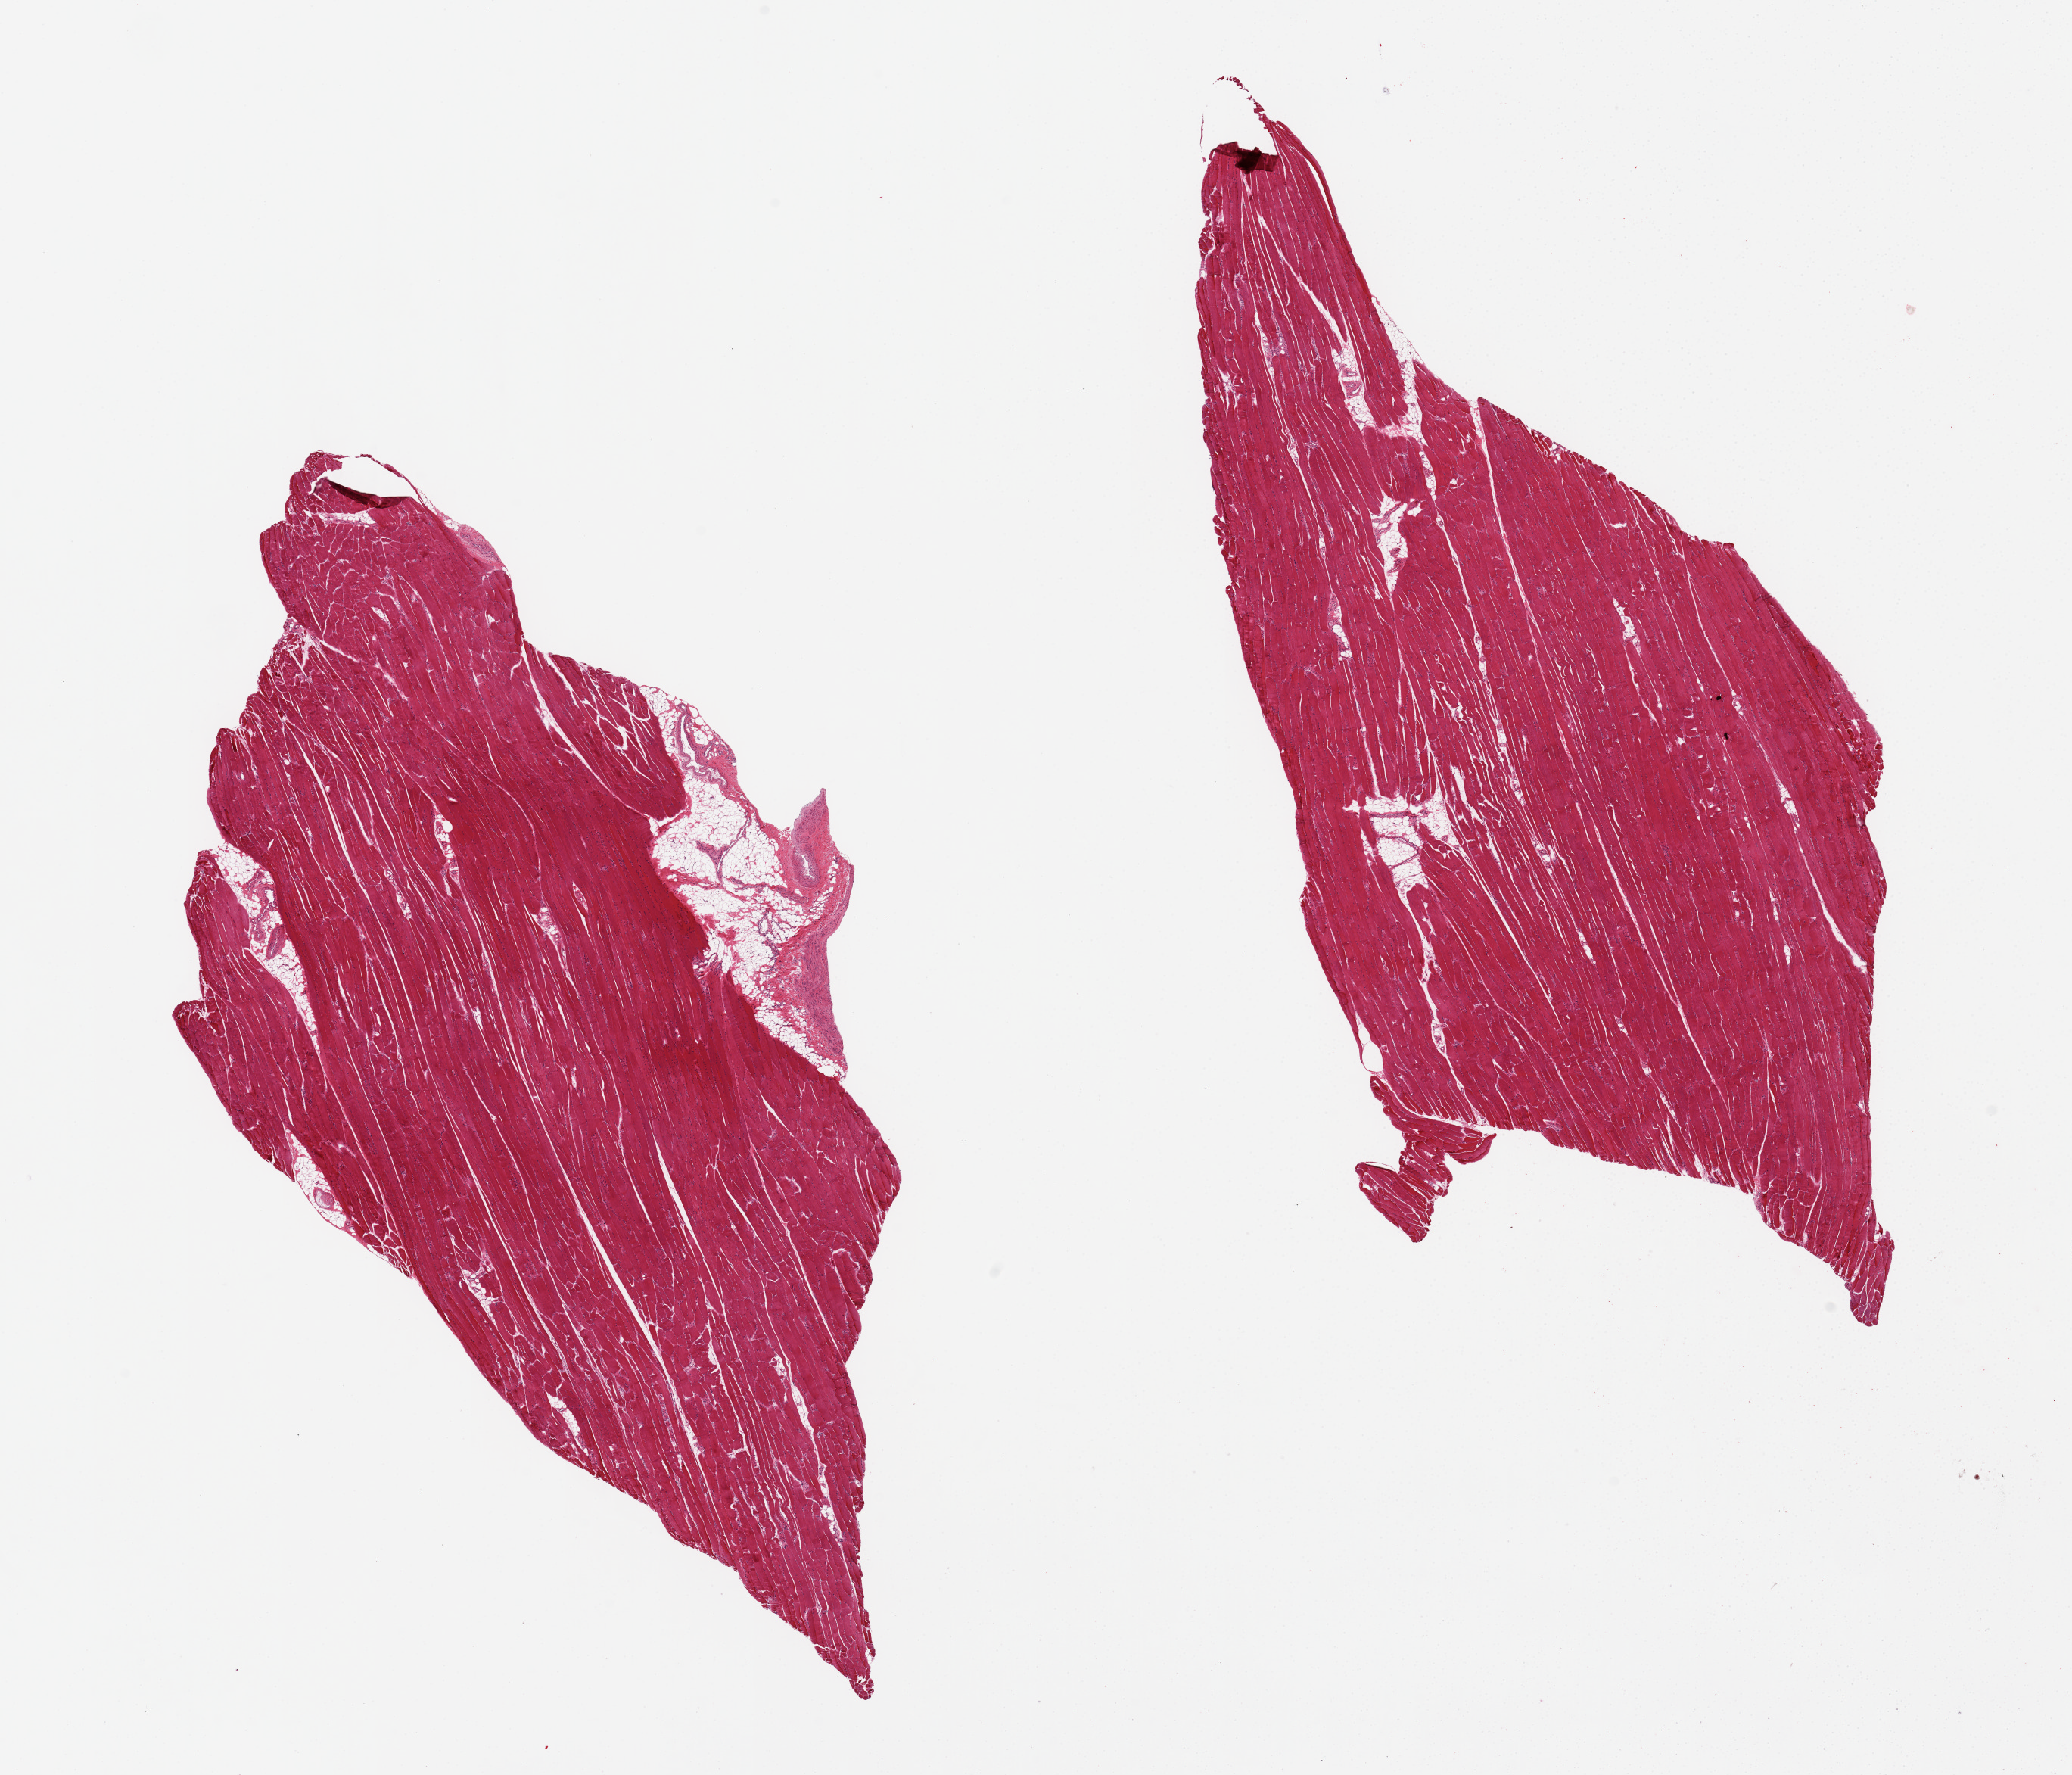
H&E whole-slide image — a low-resolution overview of the entire scanned area, about 21.7 x 18.5 mm. Female donor.
- specimen: PAXgene-fixed, paraffin-embedded tissue; section of skeletal muscle (target tissue); donor tissue sample